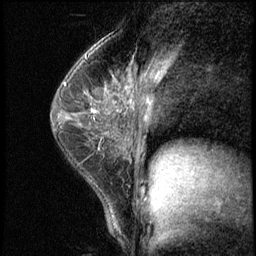
Breast MRI (dynamic contrast-enhanced), one sagittal slice; position 39 of 62 along the scan axis; 3 images stored at this slice position (order not interpretable as contrast timing); 1.5 T; TE 4.2 ms, TR 8.7 ms; 2.5 mm slice thickness; 256 × 256 image matrix, field of view 180 × 180 mm. Patient: female, 35 years. From the clinical record (not read from this slice): setting: breast cancer imaged before/during neoadjuvant chemotherapy; receptor status: HER2-positive.
Structures marked on this image (semi-automatic segmentation, software-assisted and operator-edited):
- analysis volume of interest (the breast-tissue region the enhancement analysis was run in; not a lesion): box from (x=71, y=78) to (x=120, y=139) px
- tumour enhancement mask (voxels above the 140 % enhancement threshold inside the analysis volume of interest): (x=92, y=109)–(x=95, y=111)